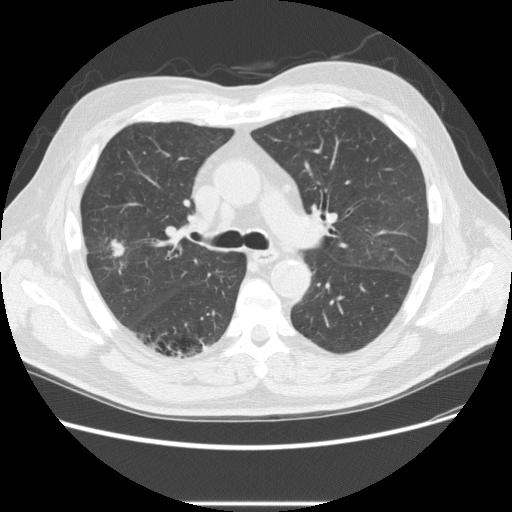
Low-dose screening chest CT, one axial slice. Position 145 of 233 along the scan axis. Reconstruction kernel STANDARD. 120 kVp. Lung window (W 1500 / L -600 HU). 512 × 512 image matrix, field of view 380 × 380 mm.
Outlined on this slice (outlined manually by an expert reader):
- lesion 2 (tumor, upper lobe of right lung): bounding box (x1, y1, x2, y2) in pixels: (110, 240, 125, 258)